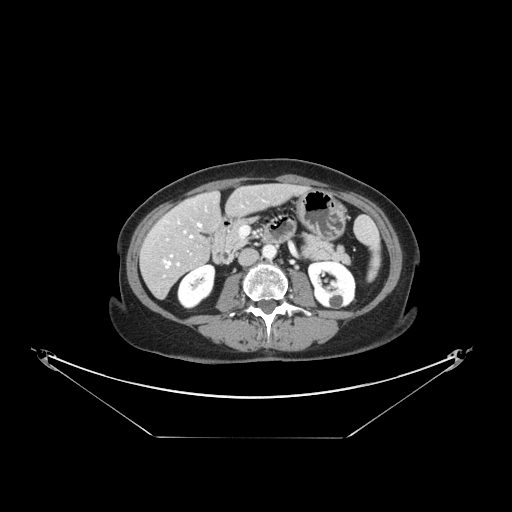
Contrast-enhanced abdominal CT, one axial slice; slice 54 of 148 in the series (ordered by position); intravenous contrast given; soft-tissue window (W 400 / L 40 HU); 2.5 mm slice thickness; 512 × 512 image matrix, field of view 500 × 500 mm. Female patient, age 73 years. From the clinical record (not read from this slice): diagnosis: colorectal cancer liver metastases, imaged before liver resection; multiple liver metastases: no; largest metastasis: 1 cm; disease in both lobes: no.
Structures marked on this image (expert manual segmentation):
- hepatic veins: bounding box (x1, y1, x2, y2) in pixels: (164, 222, 201, 268)
- liver: (143, 184, 298, 297)
- planned liver remnant (the part of the liver to remain after resection): (163, 185, 298, 248)